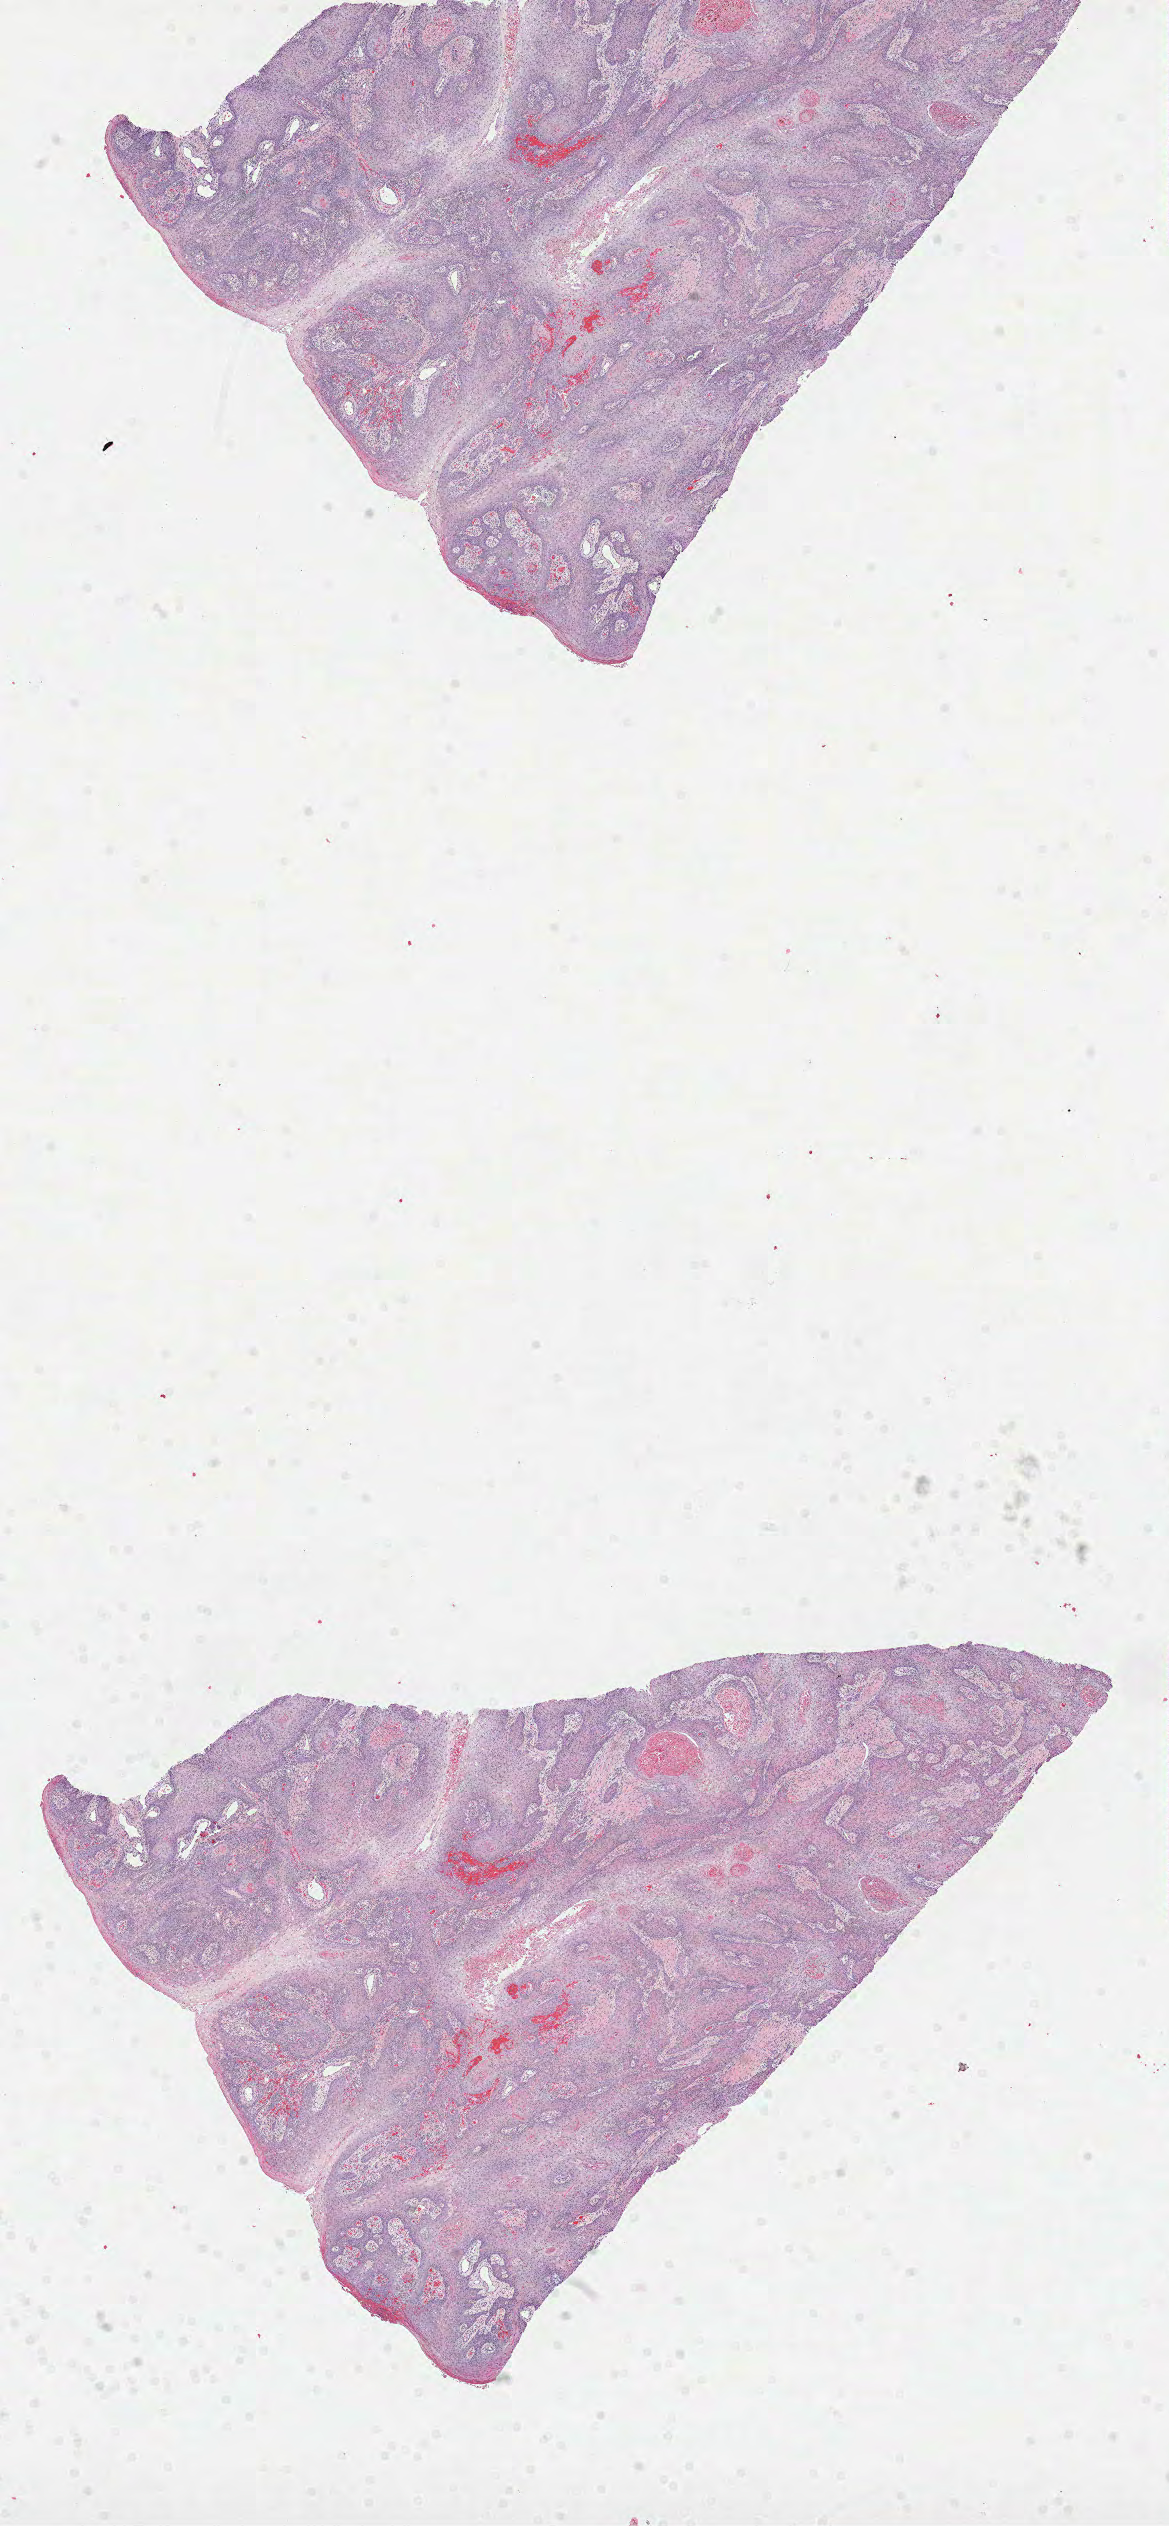
Whole-slide histology image, H&E-stained, shown as a low-resolution overview of the whole scanned area (about 9.4 x 20.4 mm, acquisition: 40x scan); formalin-fixed paraffin-embedded (FFPE) diagnostic section; sample: primary tumour, head and neck. Patient: male, age at initial diagnosis 70 years. Histologic grade: G2 (moderately differentiated).
- histologic diagnosis: Squamous cell carcinoma, NOS (cheek mucosa)
- AJCC pathologic stage: II (7th edition)